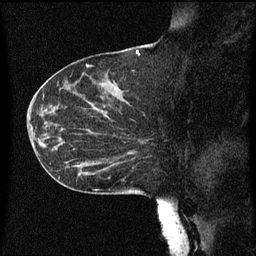
Breast MRI (dynamic contrast-enhanced), one sagittal slice; slice 30 of 60 in the series (ordered by position); dynamic contrast-enhanced series, image 2 of 3 at this slice position (ordered by acquisition); 1.5 T; TE 4.2 ms, TR 8 ms; 2 mm slice thickness; 256 × 256 image matrix. Patient: female, 55 years.
Outlined on this slice (semi-automatic segmentation, software-assisted and operator-edited):
- analysis volume of interest (the breast-tissue region the enhancement analysis was run in; not a lesion): box from (x=46, y=124) to (x=151, y=183) px
- tumour enhancement mask (voxels above the 70 % enhancement threshold inside the analysis volume of interest): (x=92, y=152)–(x=135, y=163)